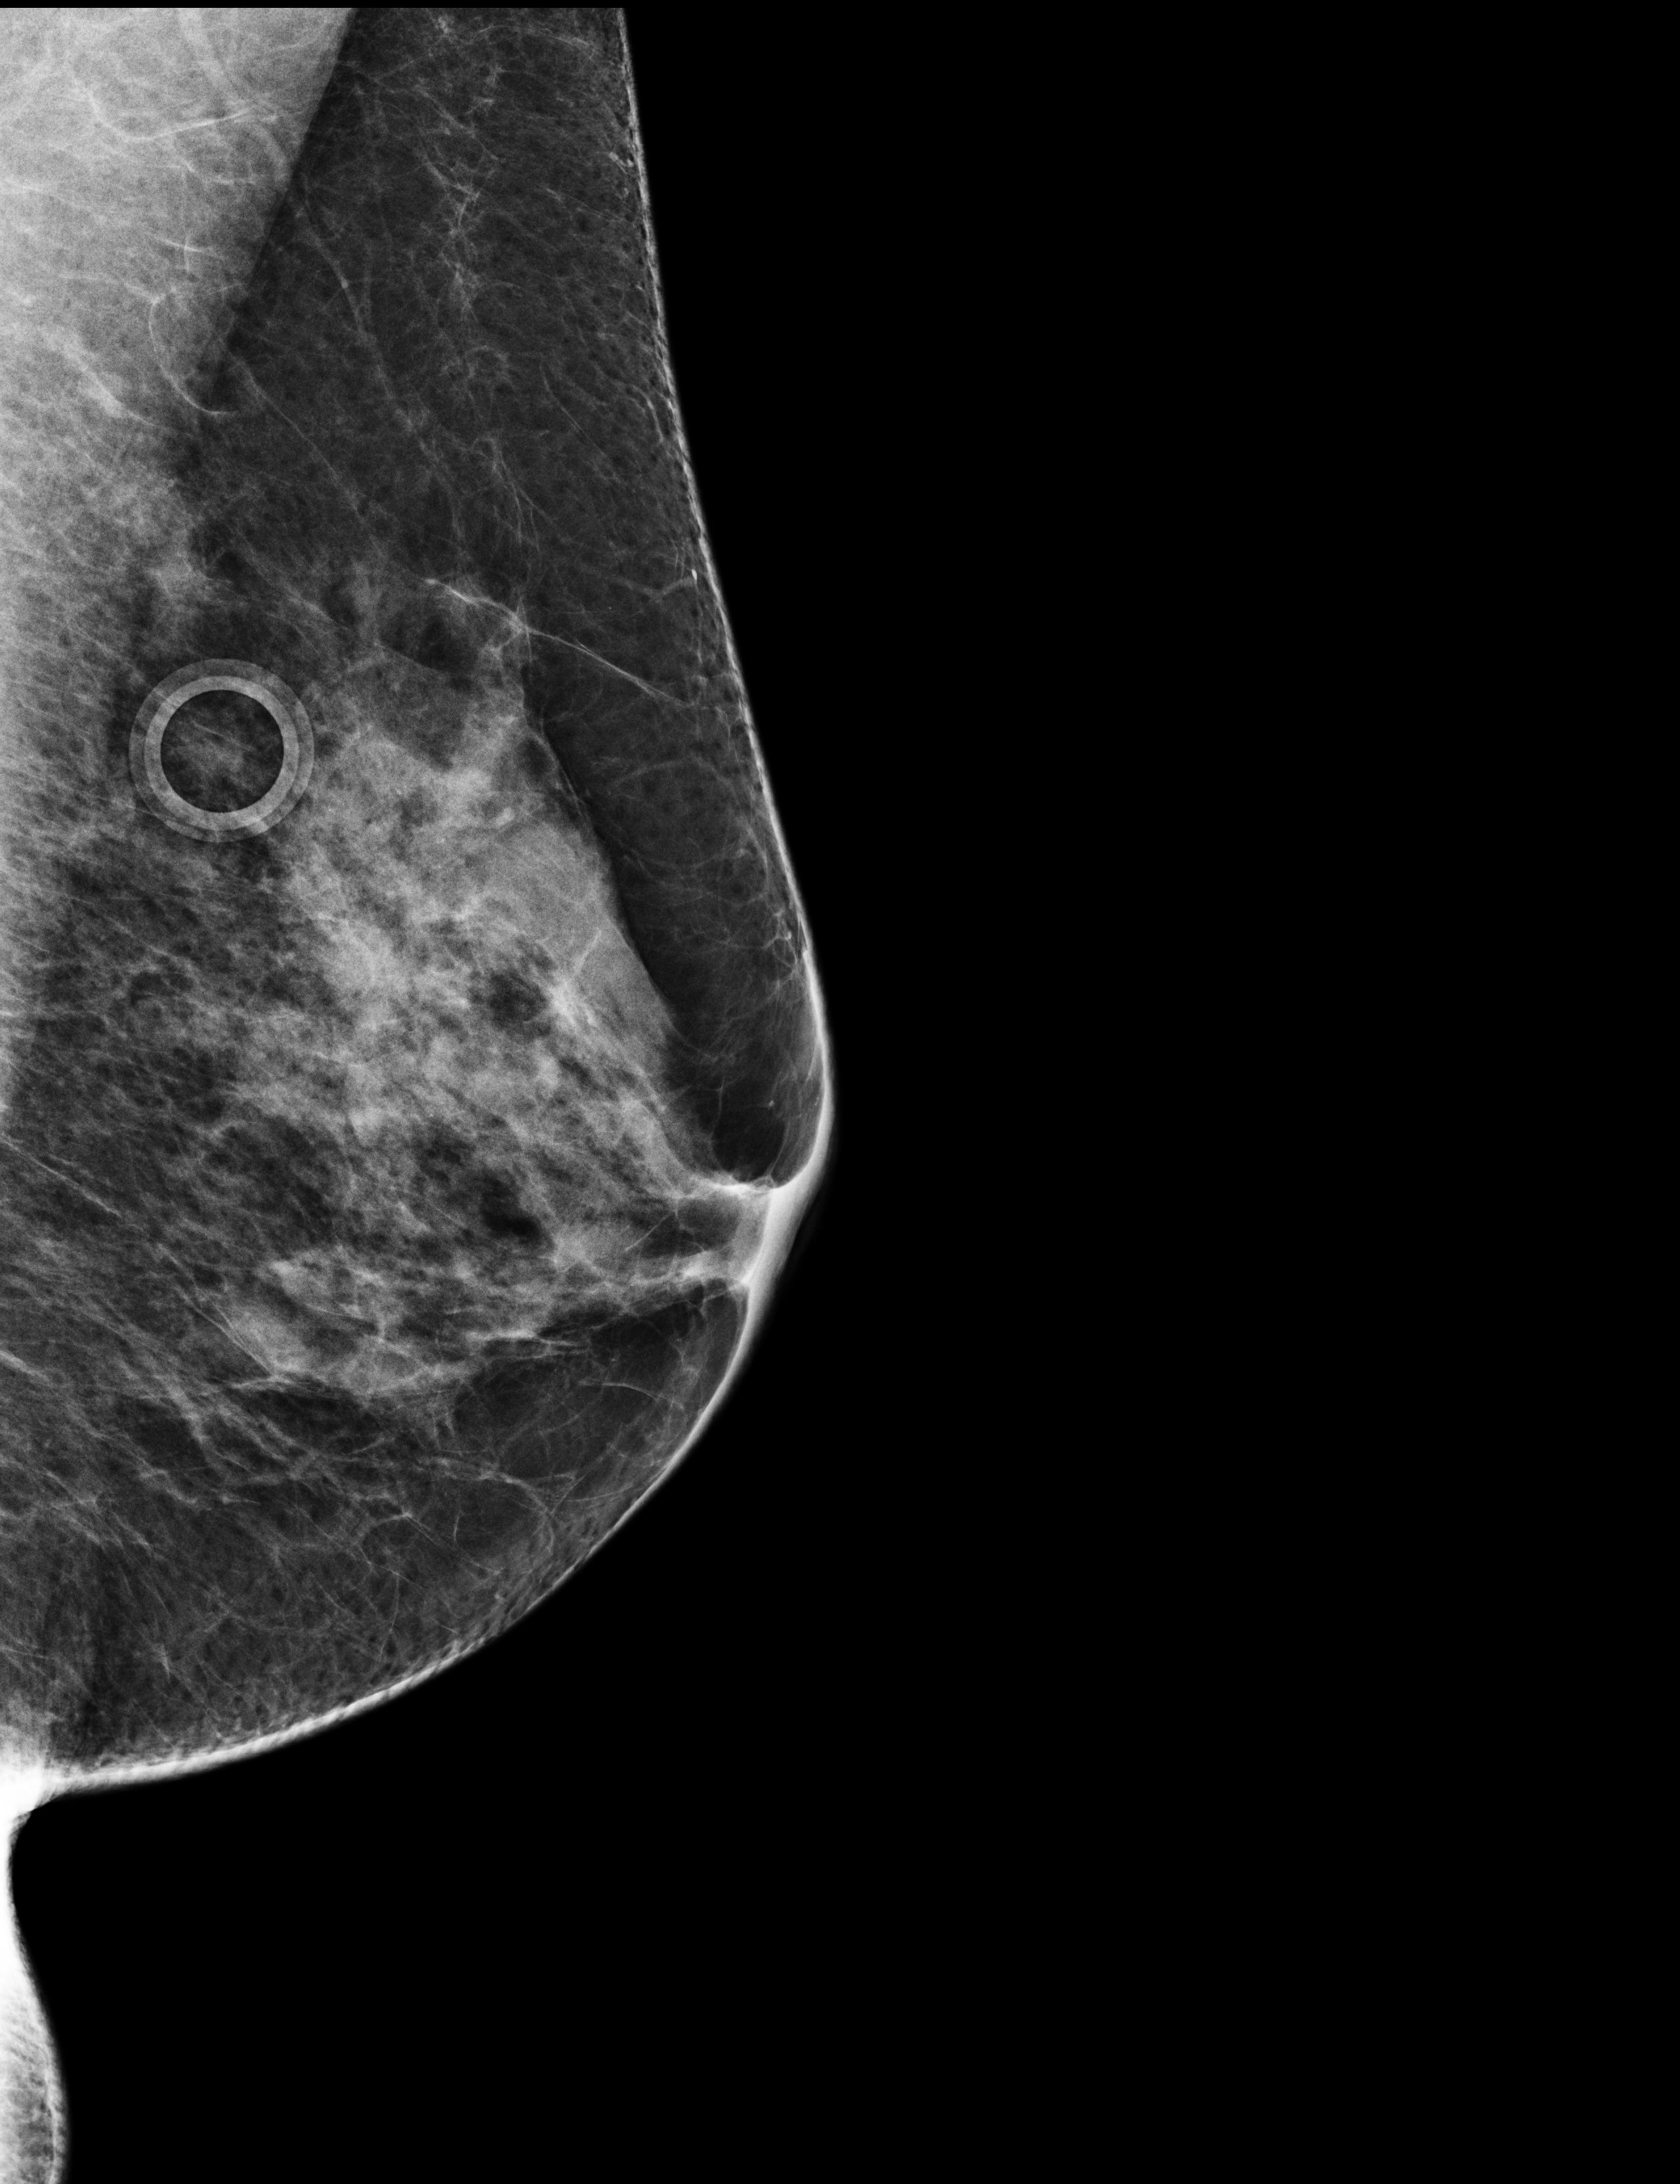
Screening examination; system: Selenia Dimensions. Patient: female, 59 years.
Image type: full-field digital mammogram. Breast: left. Projection: medio-lateral oblique projection.